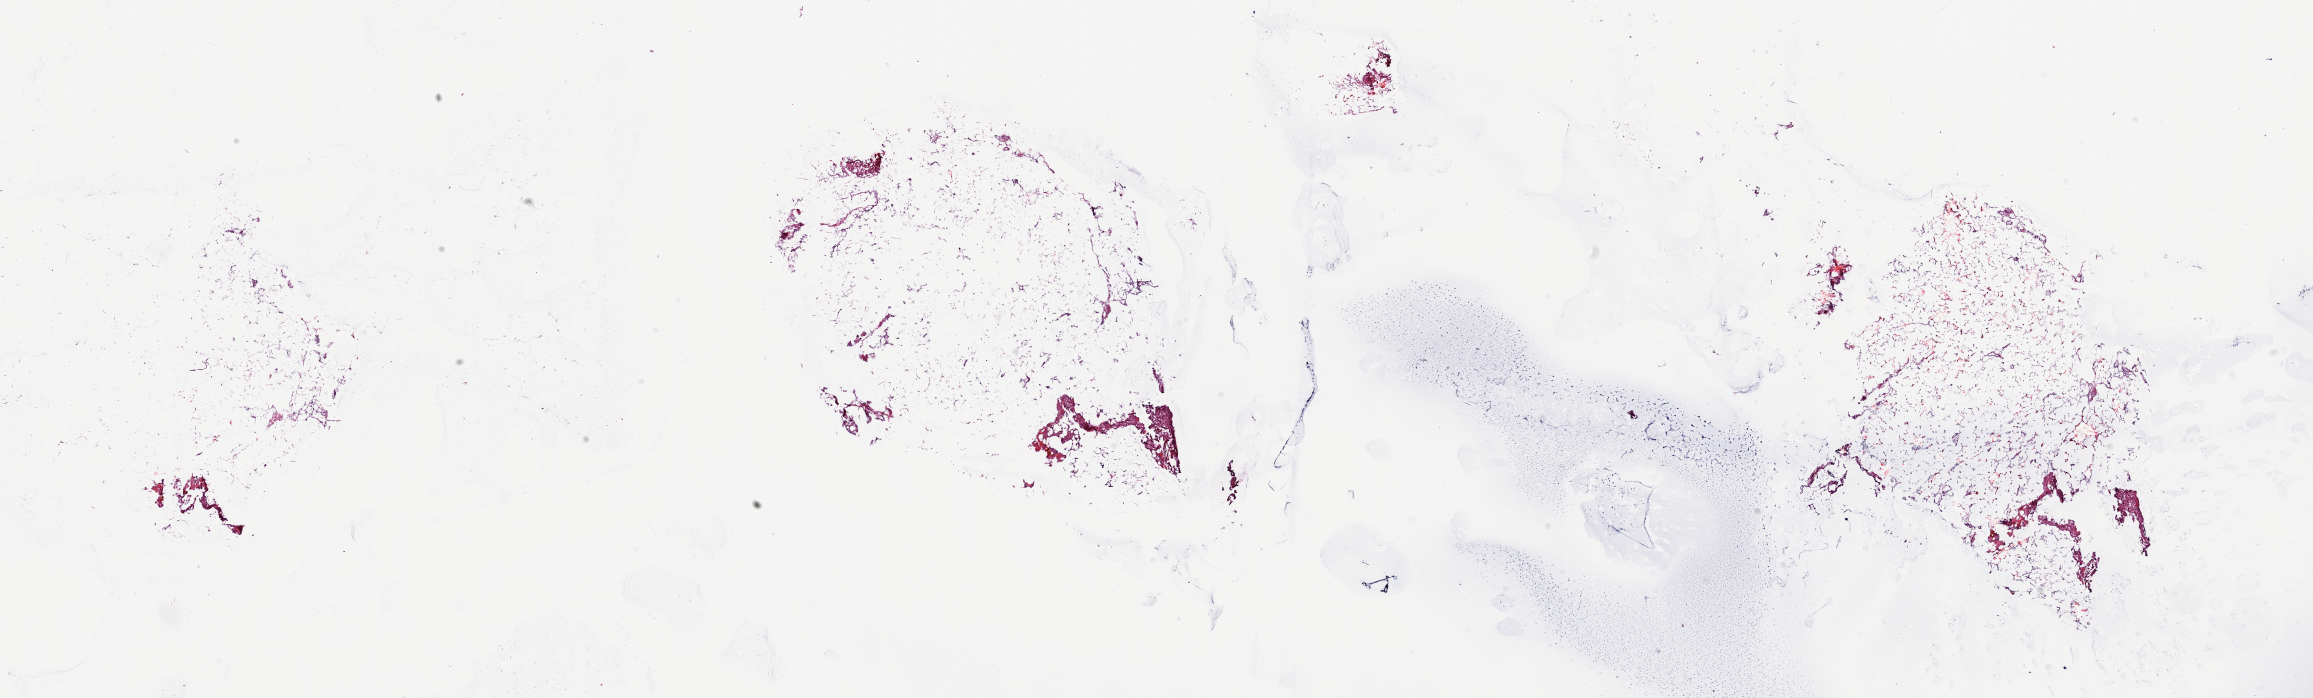
H&E whole-slide image — a low-resolution overview of the entire scanned area, about 36.7 x 11.1 mm (acquisition: 20x scan); frozen section from the top of the tissue portion; sample: solid tissue normal (non-tumour tissue), thymus. Female patient; age at initial diagnosis 76 years. Slide review estimates, as recorded: tumour cells 0%, tumour nuclei 0%, normal cells 96%, stromal cells 4%, necrosis 0%. Inflammatory infiltration, as recorded: lymphocyte infiltration 5%, monocyte infiltration 0%, neutrophil infiltration 0%.
- this section: solid tissue normal sample (biorepository sample class)
- patient diagnosis: Thymoma, type A, malignant